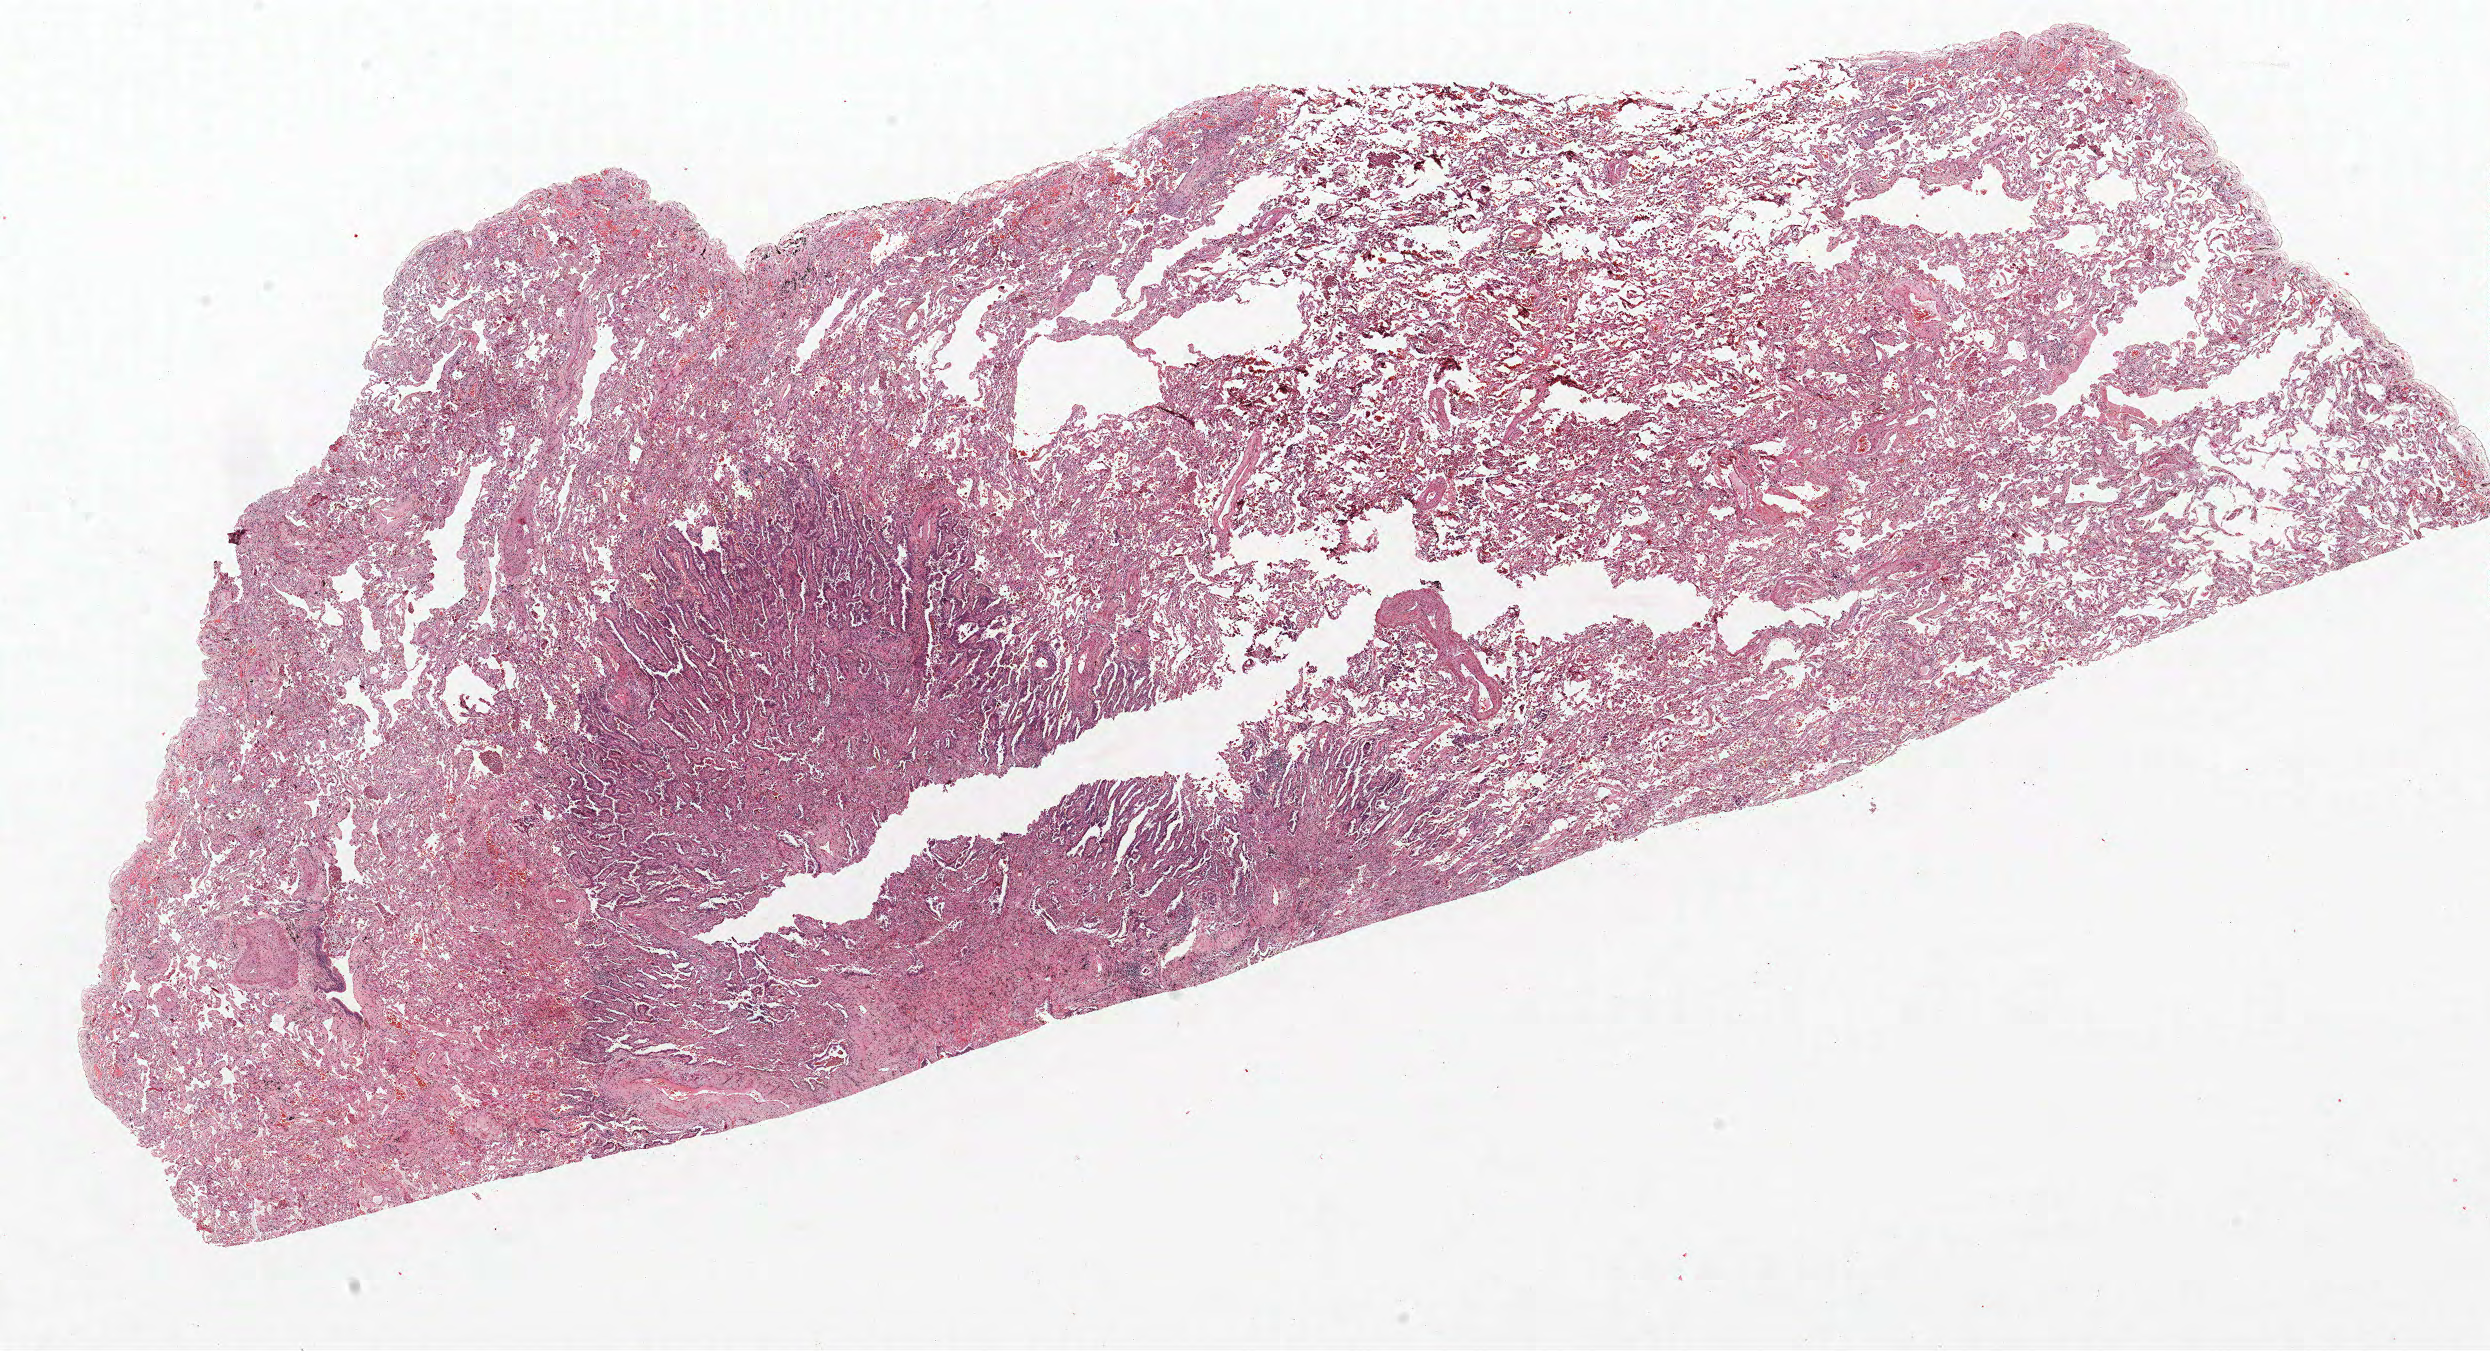
Hematoxylin and eosin (H&E) stained whole-slide image, a low-resolution overview of the entire scanned area, about 19.9 x 10.8 mm. Formalin-fixed paraffin-embedded (FFPE) section. Lung tissue. Female patient, aged 55 at enrolment. Current smoker at enrolment.
Participant's lung-cancer diagnosis: Bronchiolo-alveolar adenocarcinoma, NOS (ICD-O-3 8250/3).